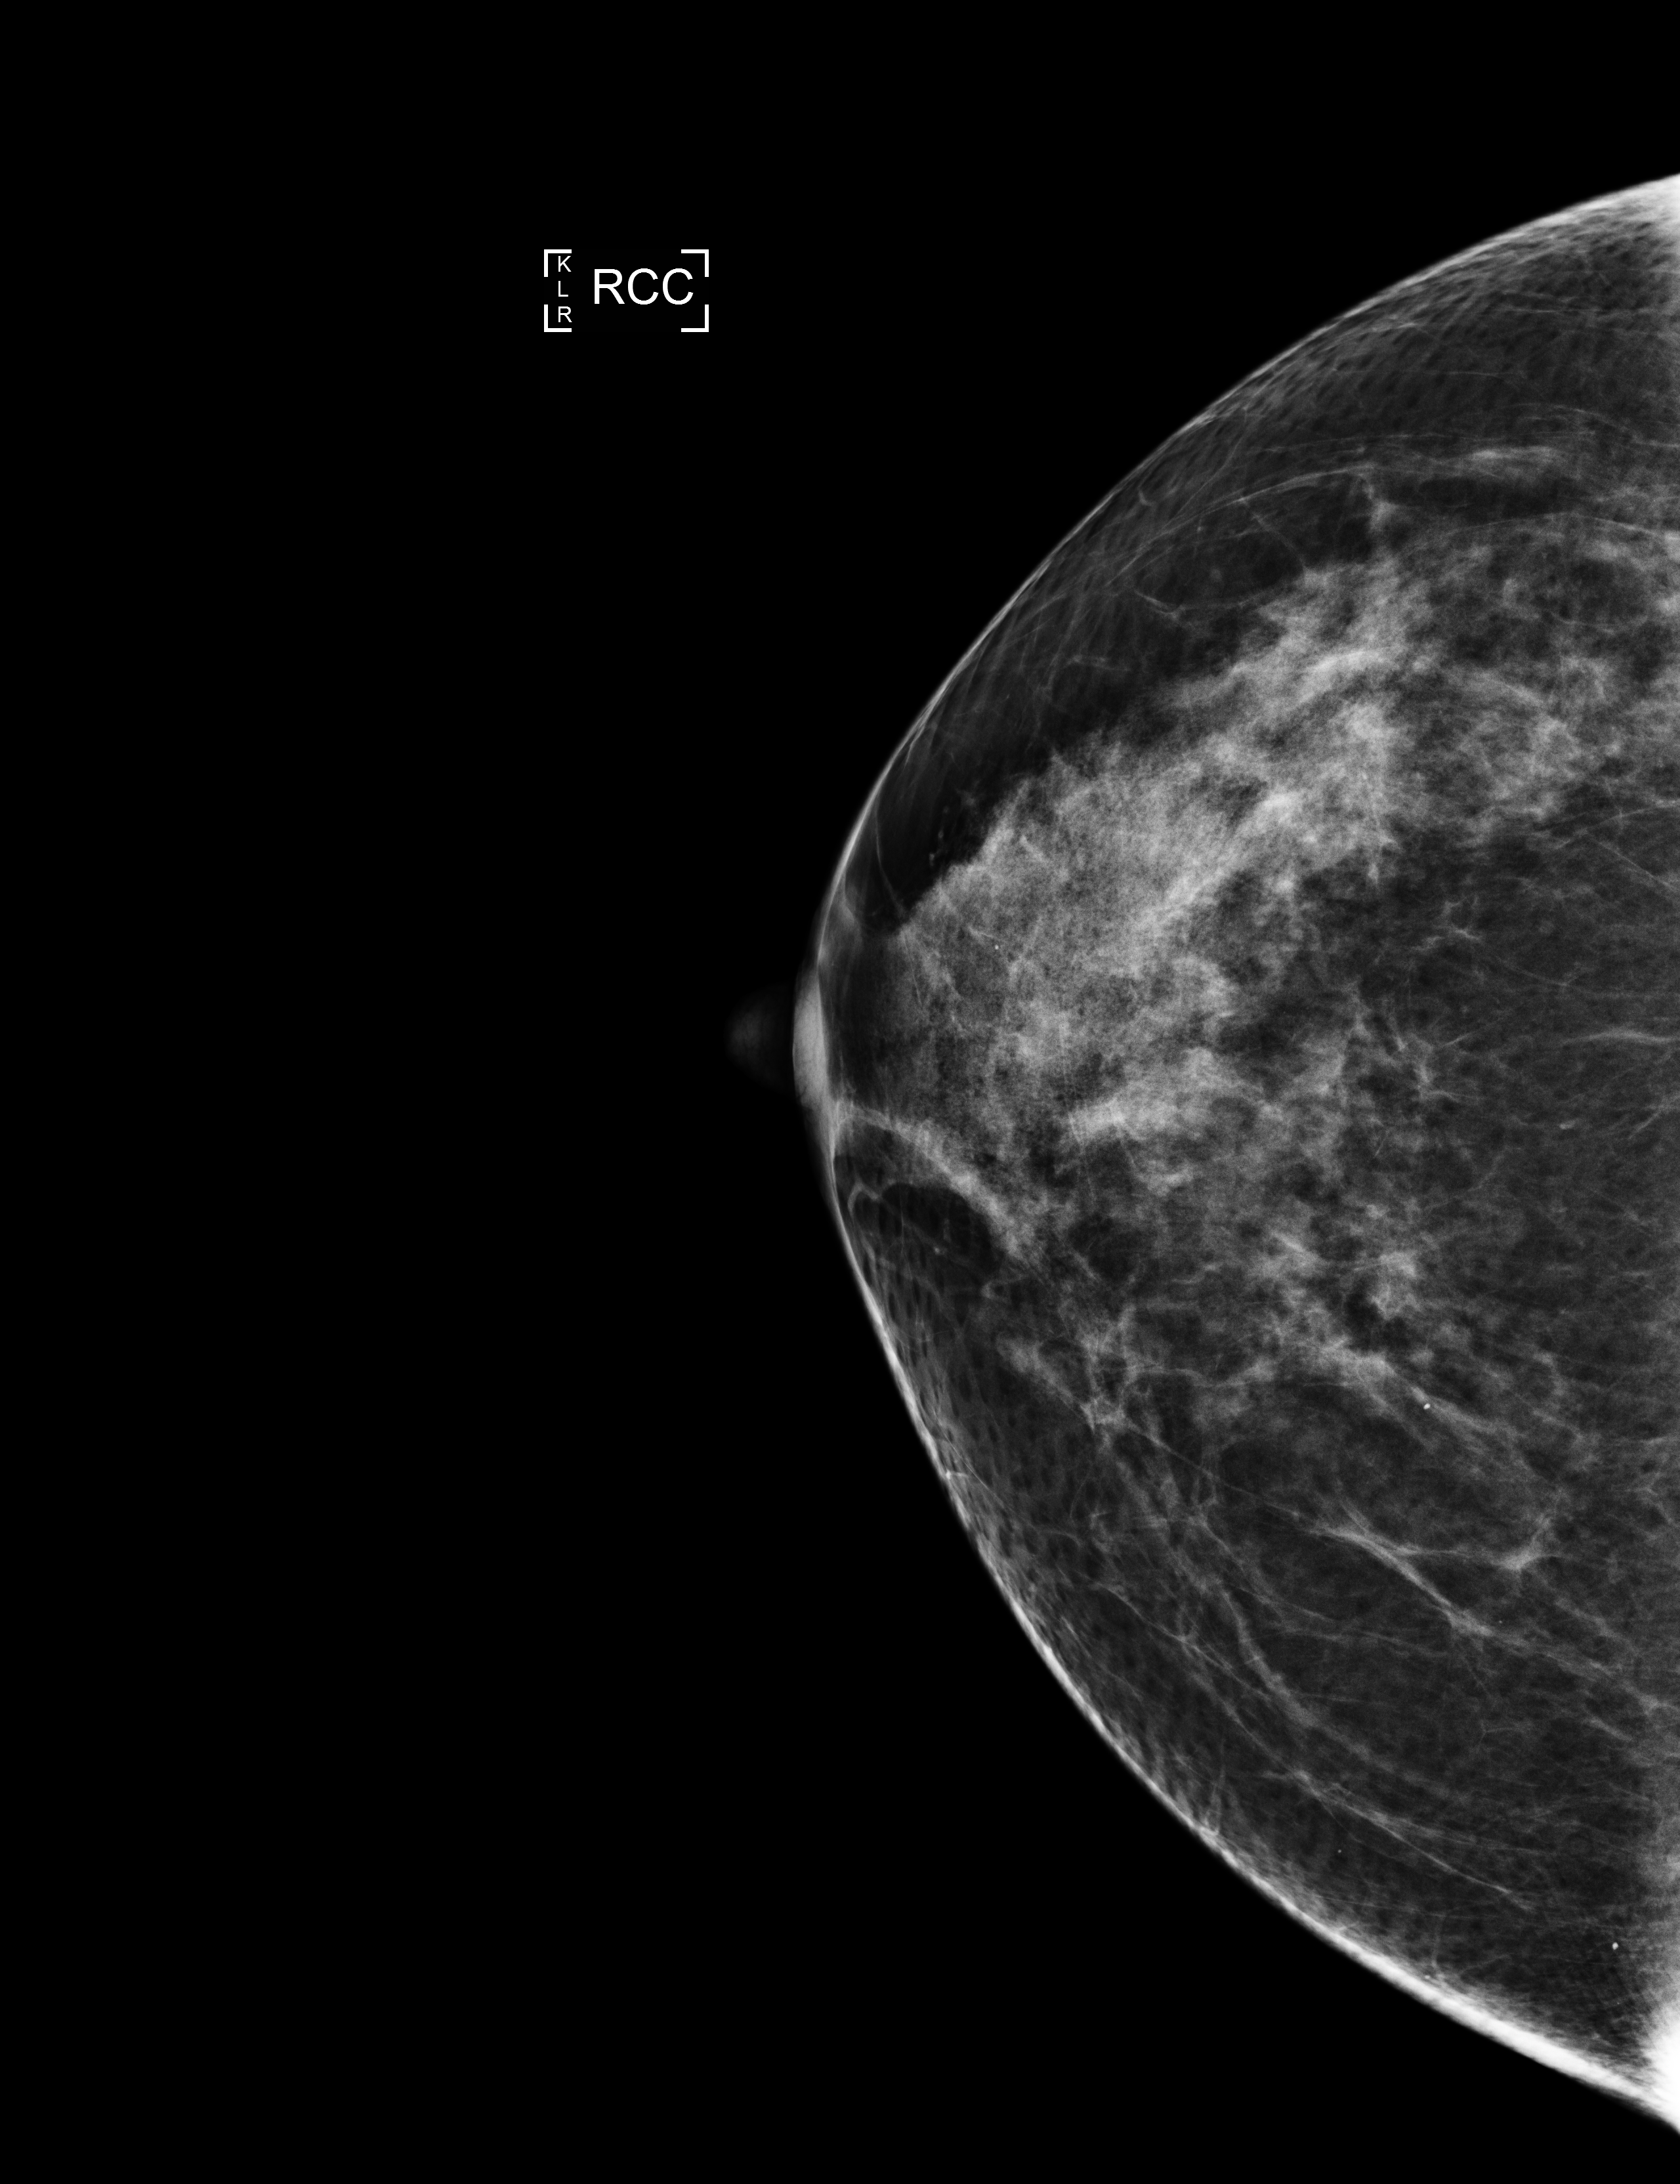
Screening examination. Female patient, age 51 years.
Image type: full-field digital mammogram. Breast: right. Projection: CC view.